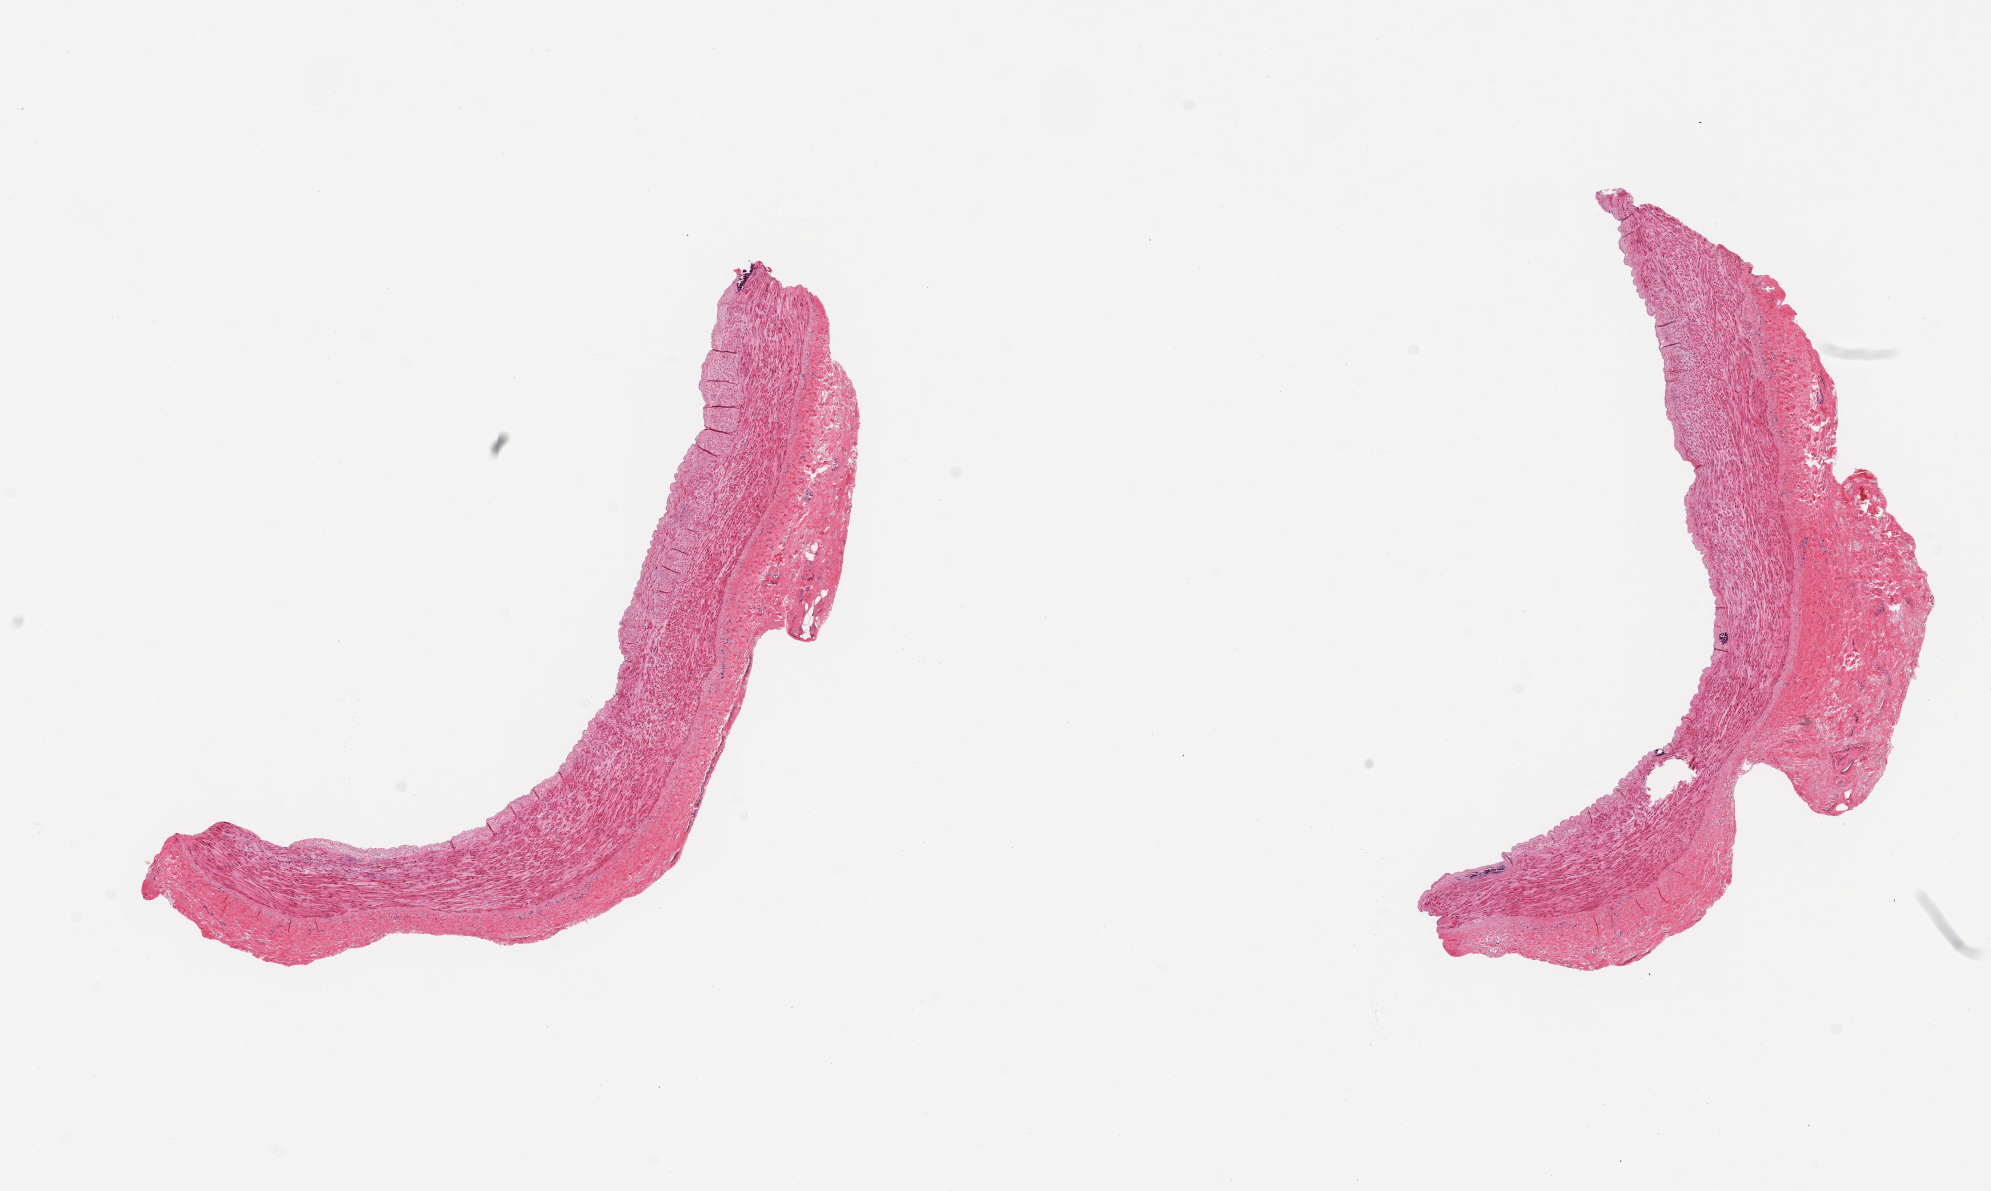
Digitized haematoxylin and eosin-stained section — shown as a low-resolution overview of the whole scanned area (about 15.8 x 9.4 mm). PAXgene-fixed, paraffin-embedded tissue. Section of tibial artery (target tissue). Tissue donor sample.
Pathologist's review note for this sample: 2 pieces; small focal calcifications; adventitia up to 1mm thick.